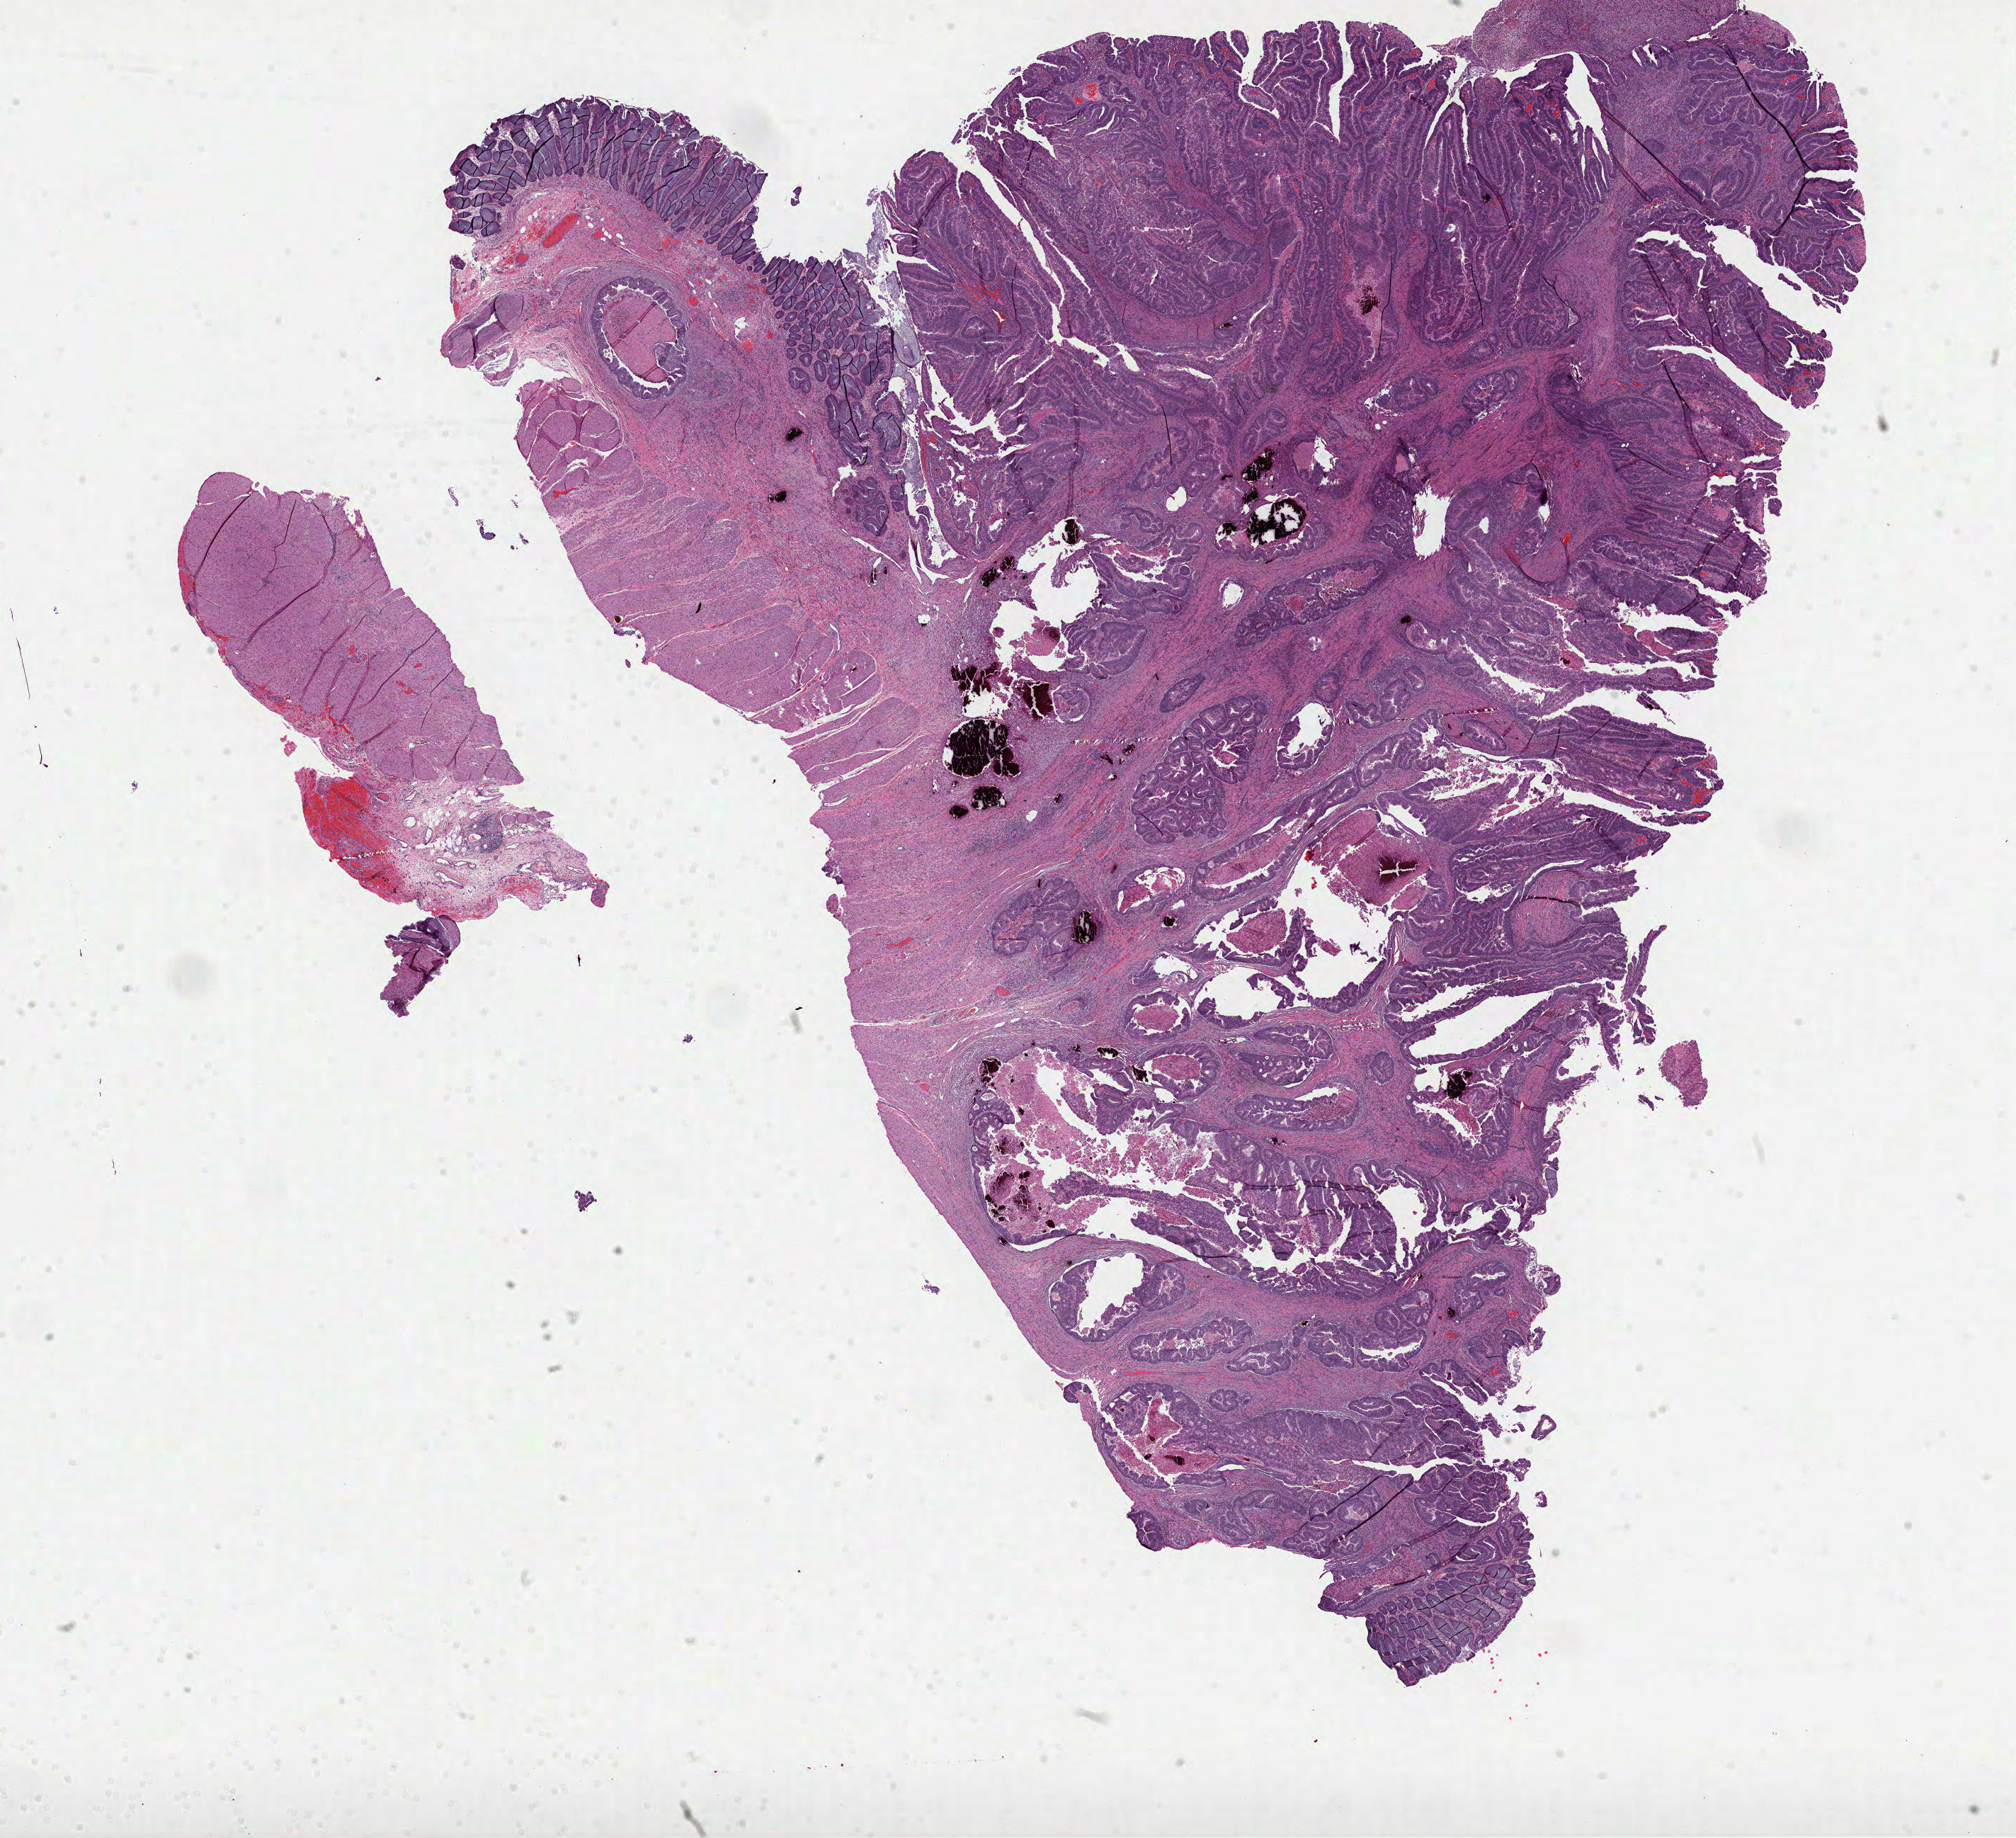
H&E whole-slide image — shown as a low-resolution overview of the whole scanned area (about 23.0 x 20.9 mm, slide scanned at 40x). FFPE section. Primary tumour sample from the colon. Male patient; age at initial diagnosis 82 years.
Histologic diagnosis: Adenocarcinoma, NOS (sigmoid colon). AJCC pathologic stage: I (7th edition). Lymph nodes positive (case pathology): 0 of 17 examined.